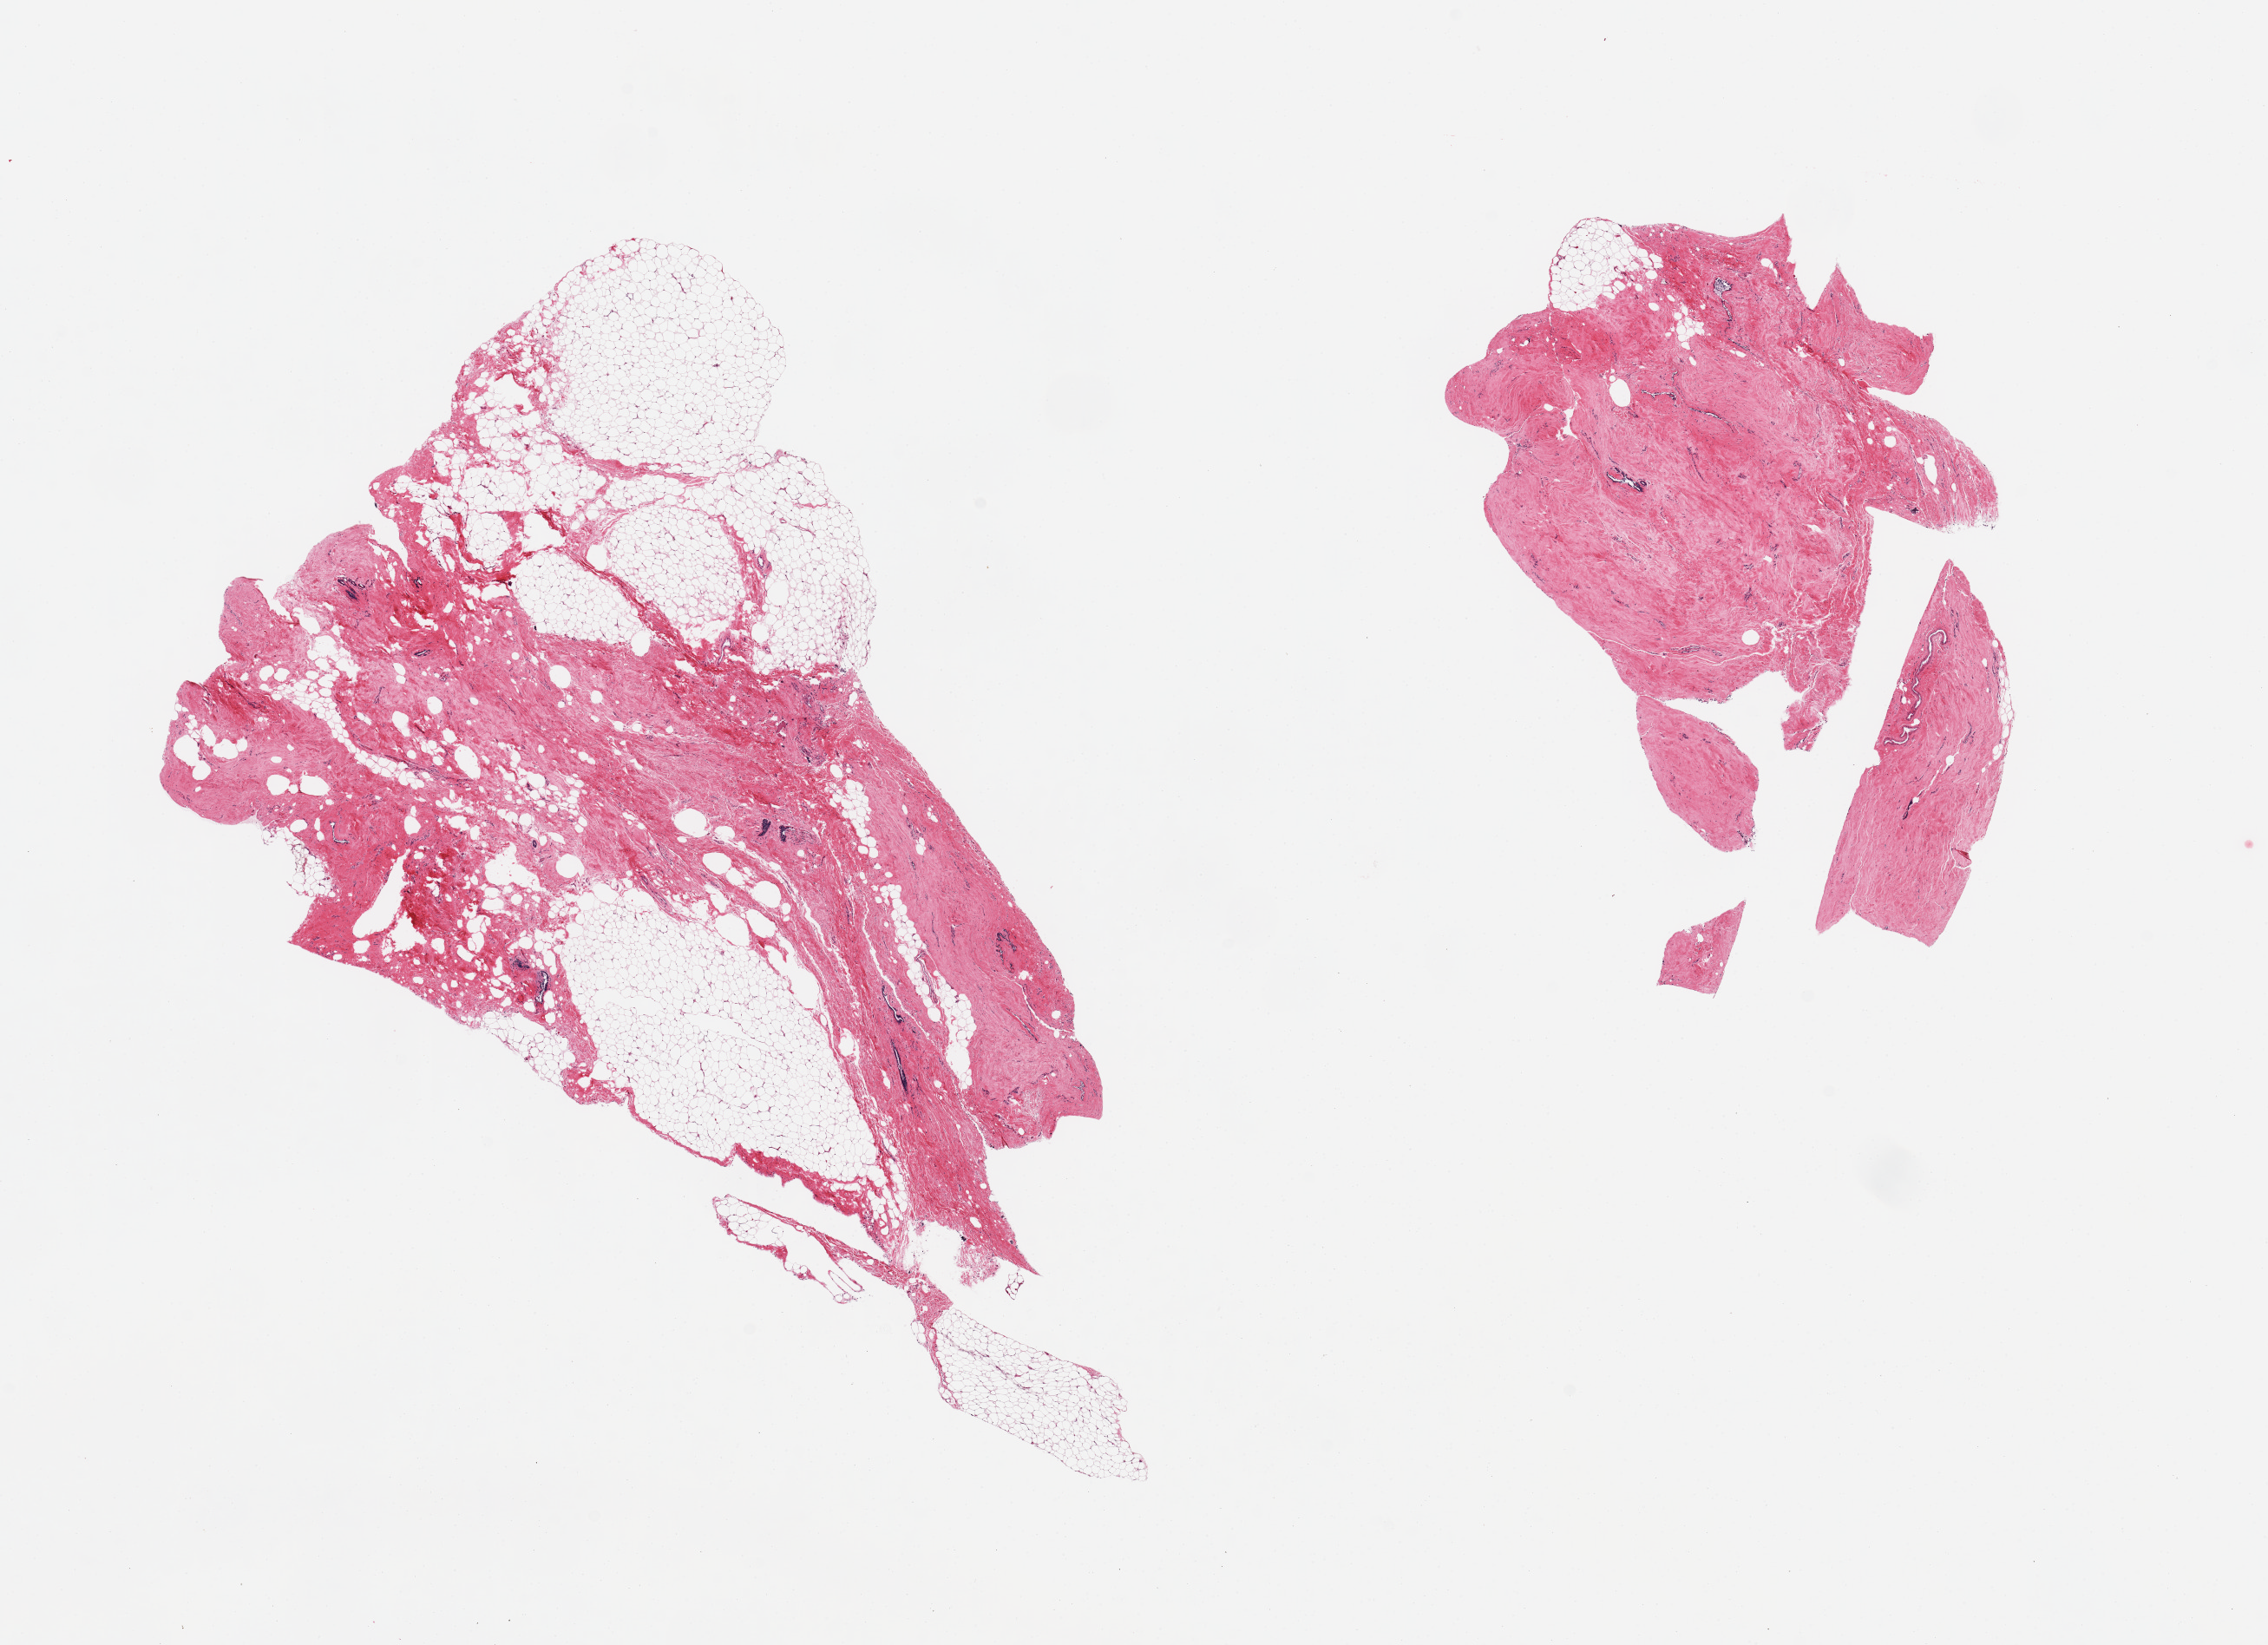
Haematoxylin and eosin whole-slide image, brightfield — a low-resolution overview of the entire scanned area, about 20.7 x 15.0 mm. PAXgene-fixed, paraffin-embedded tissue. Target tissue: breast. Tissue donor sample. Donor sex: male.
Pathologist's review note for this sample: 2 pieces, prominent gynecomastoid stromal hyperplasia; trace ductal elements present.